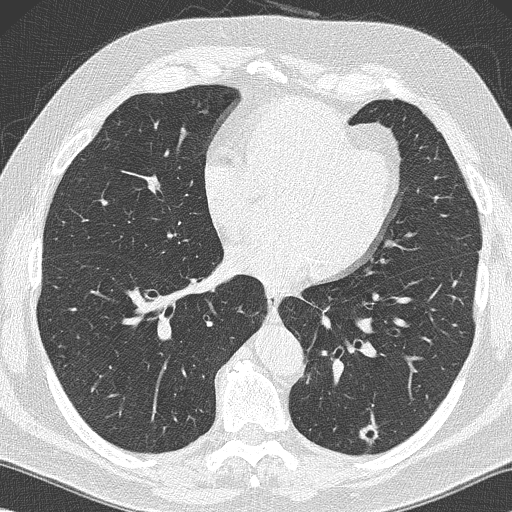
Chest CT (low-dose screening protocol), one axial image, first (baseline) screen, lung window (W 1500 / L -600 HU), 2 mm slice thickness, 120 kVp, 512 × 512 image matrix. Male, age 59 years at enrolment. Former smoker at enrolment.
- Lesion marked by an expert reader, bounding box <346,415,389,452> (left, top, right, bottom; pixels).
- The screening reader recorded 2 non-calcified nodules or masses ≥4 mm on this exam; which of them this box marks is not recorded.
- Official screen result: positive, change unspecified: nodule(s) >= 4 mm or enlarging nodule(s), mass(es), or other non-specific abnormalities suspicious for lung cancer.
- Lung cancer was diagnosed 61 days after this screen: large cell carcinoma, NOS, left lower lobe, poorly differentiated (G3), stage IA (AJCC 6th edition), 14 mm at pathology.